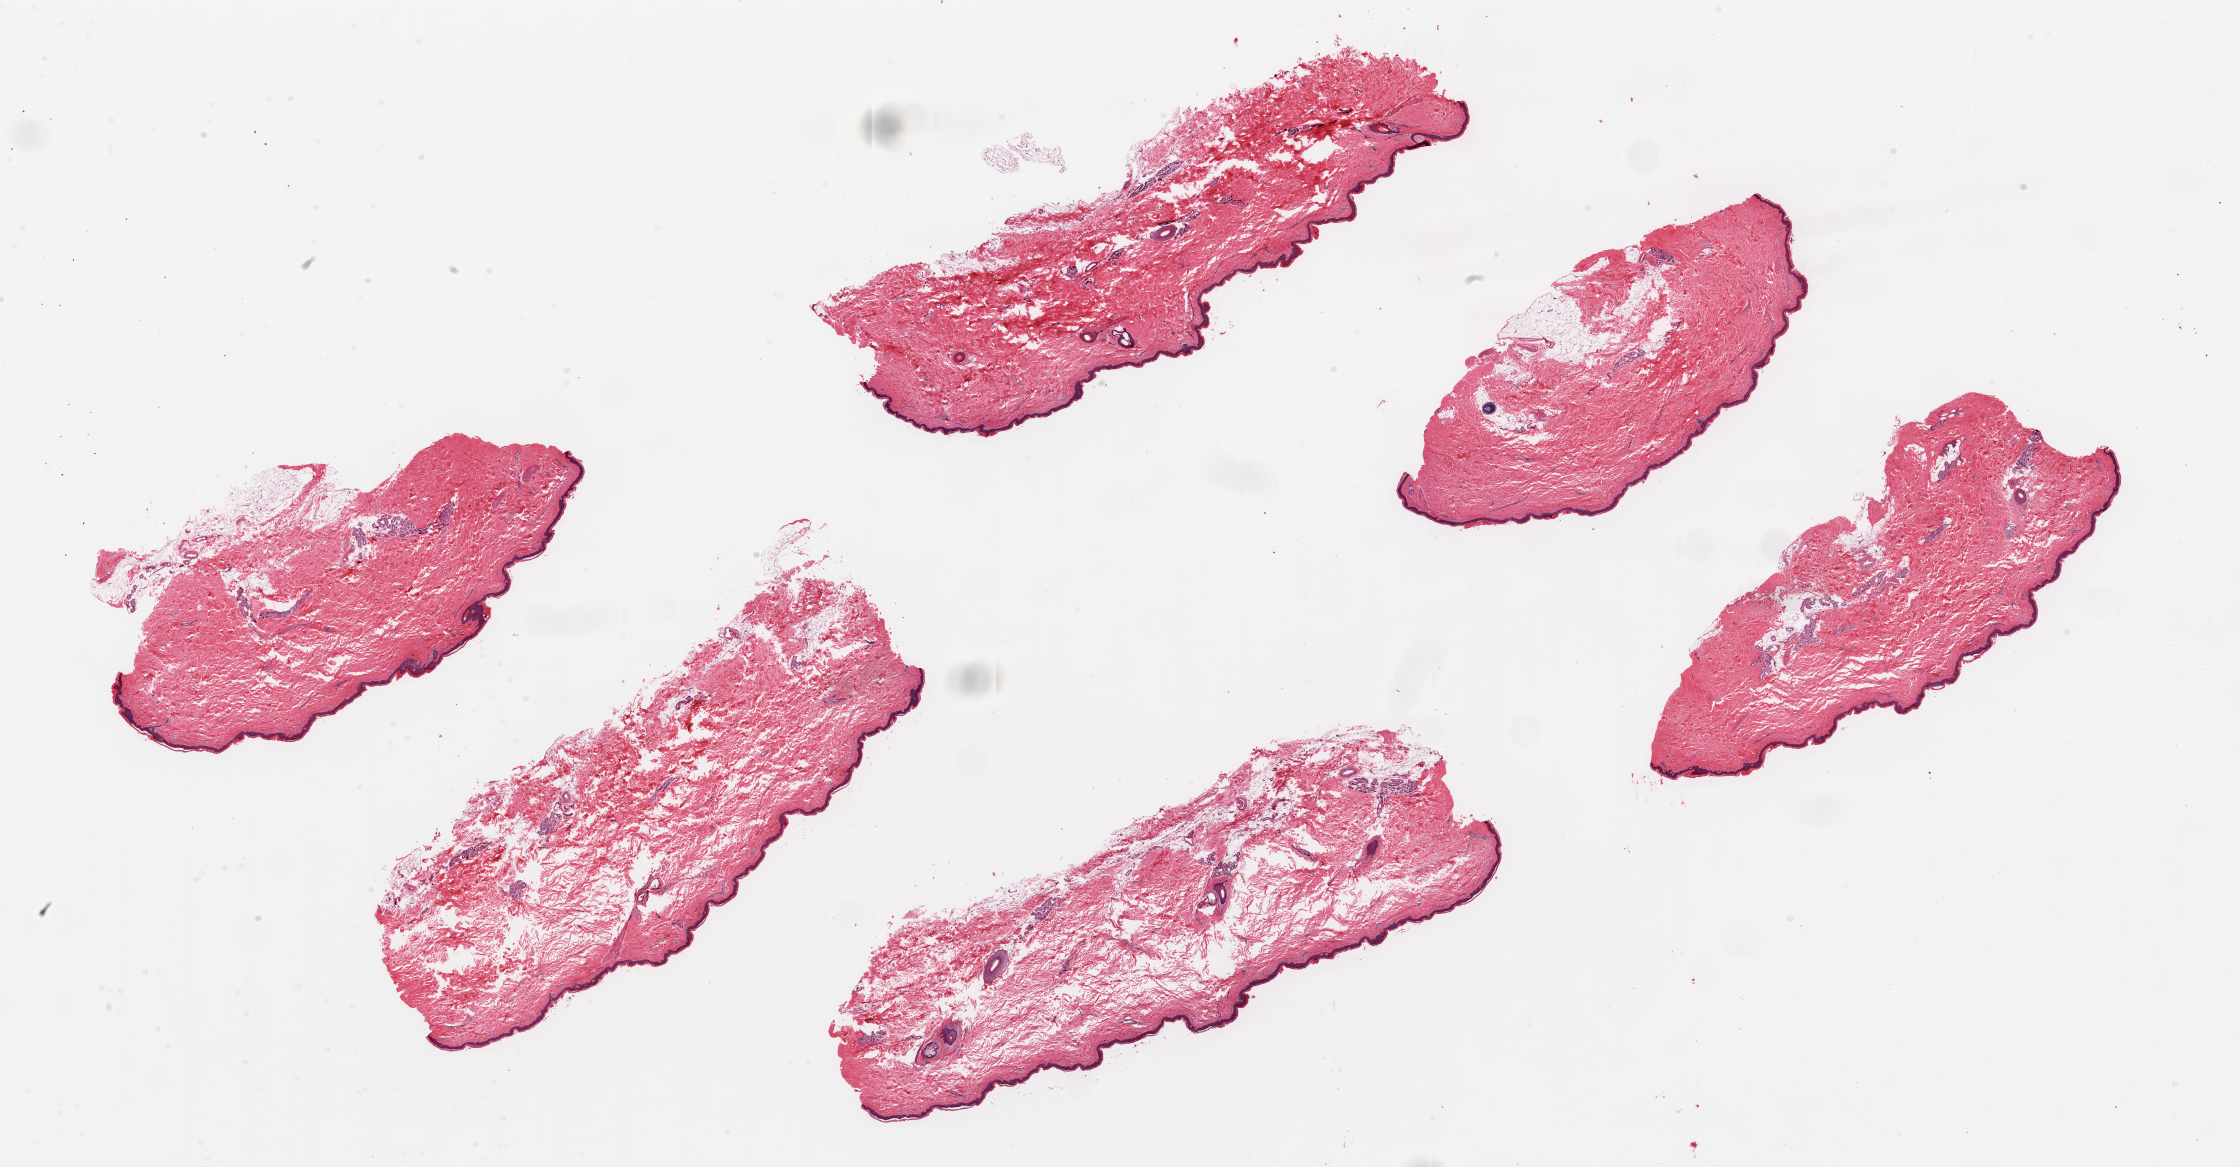
Digitized haematoxylin and eosin-stained section, a low-resolution overview of the entire scanned area, about 35.4 x 18.5 mm; PAXgene-fixed, paraffin-embedded tissue; section of skin of lower leg (target tissue); donor tissue sample. Donor: male.
- pathologist's review note for this sample: 6 ~10x3.7 mm (maximum) pieces. Fragmented dermis in 2 pieces (poor fixation)